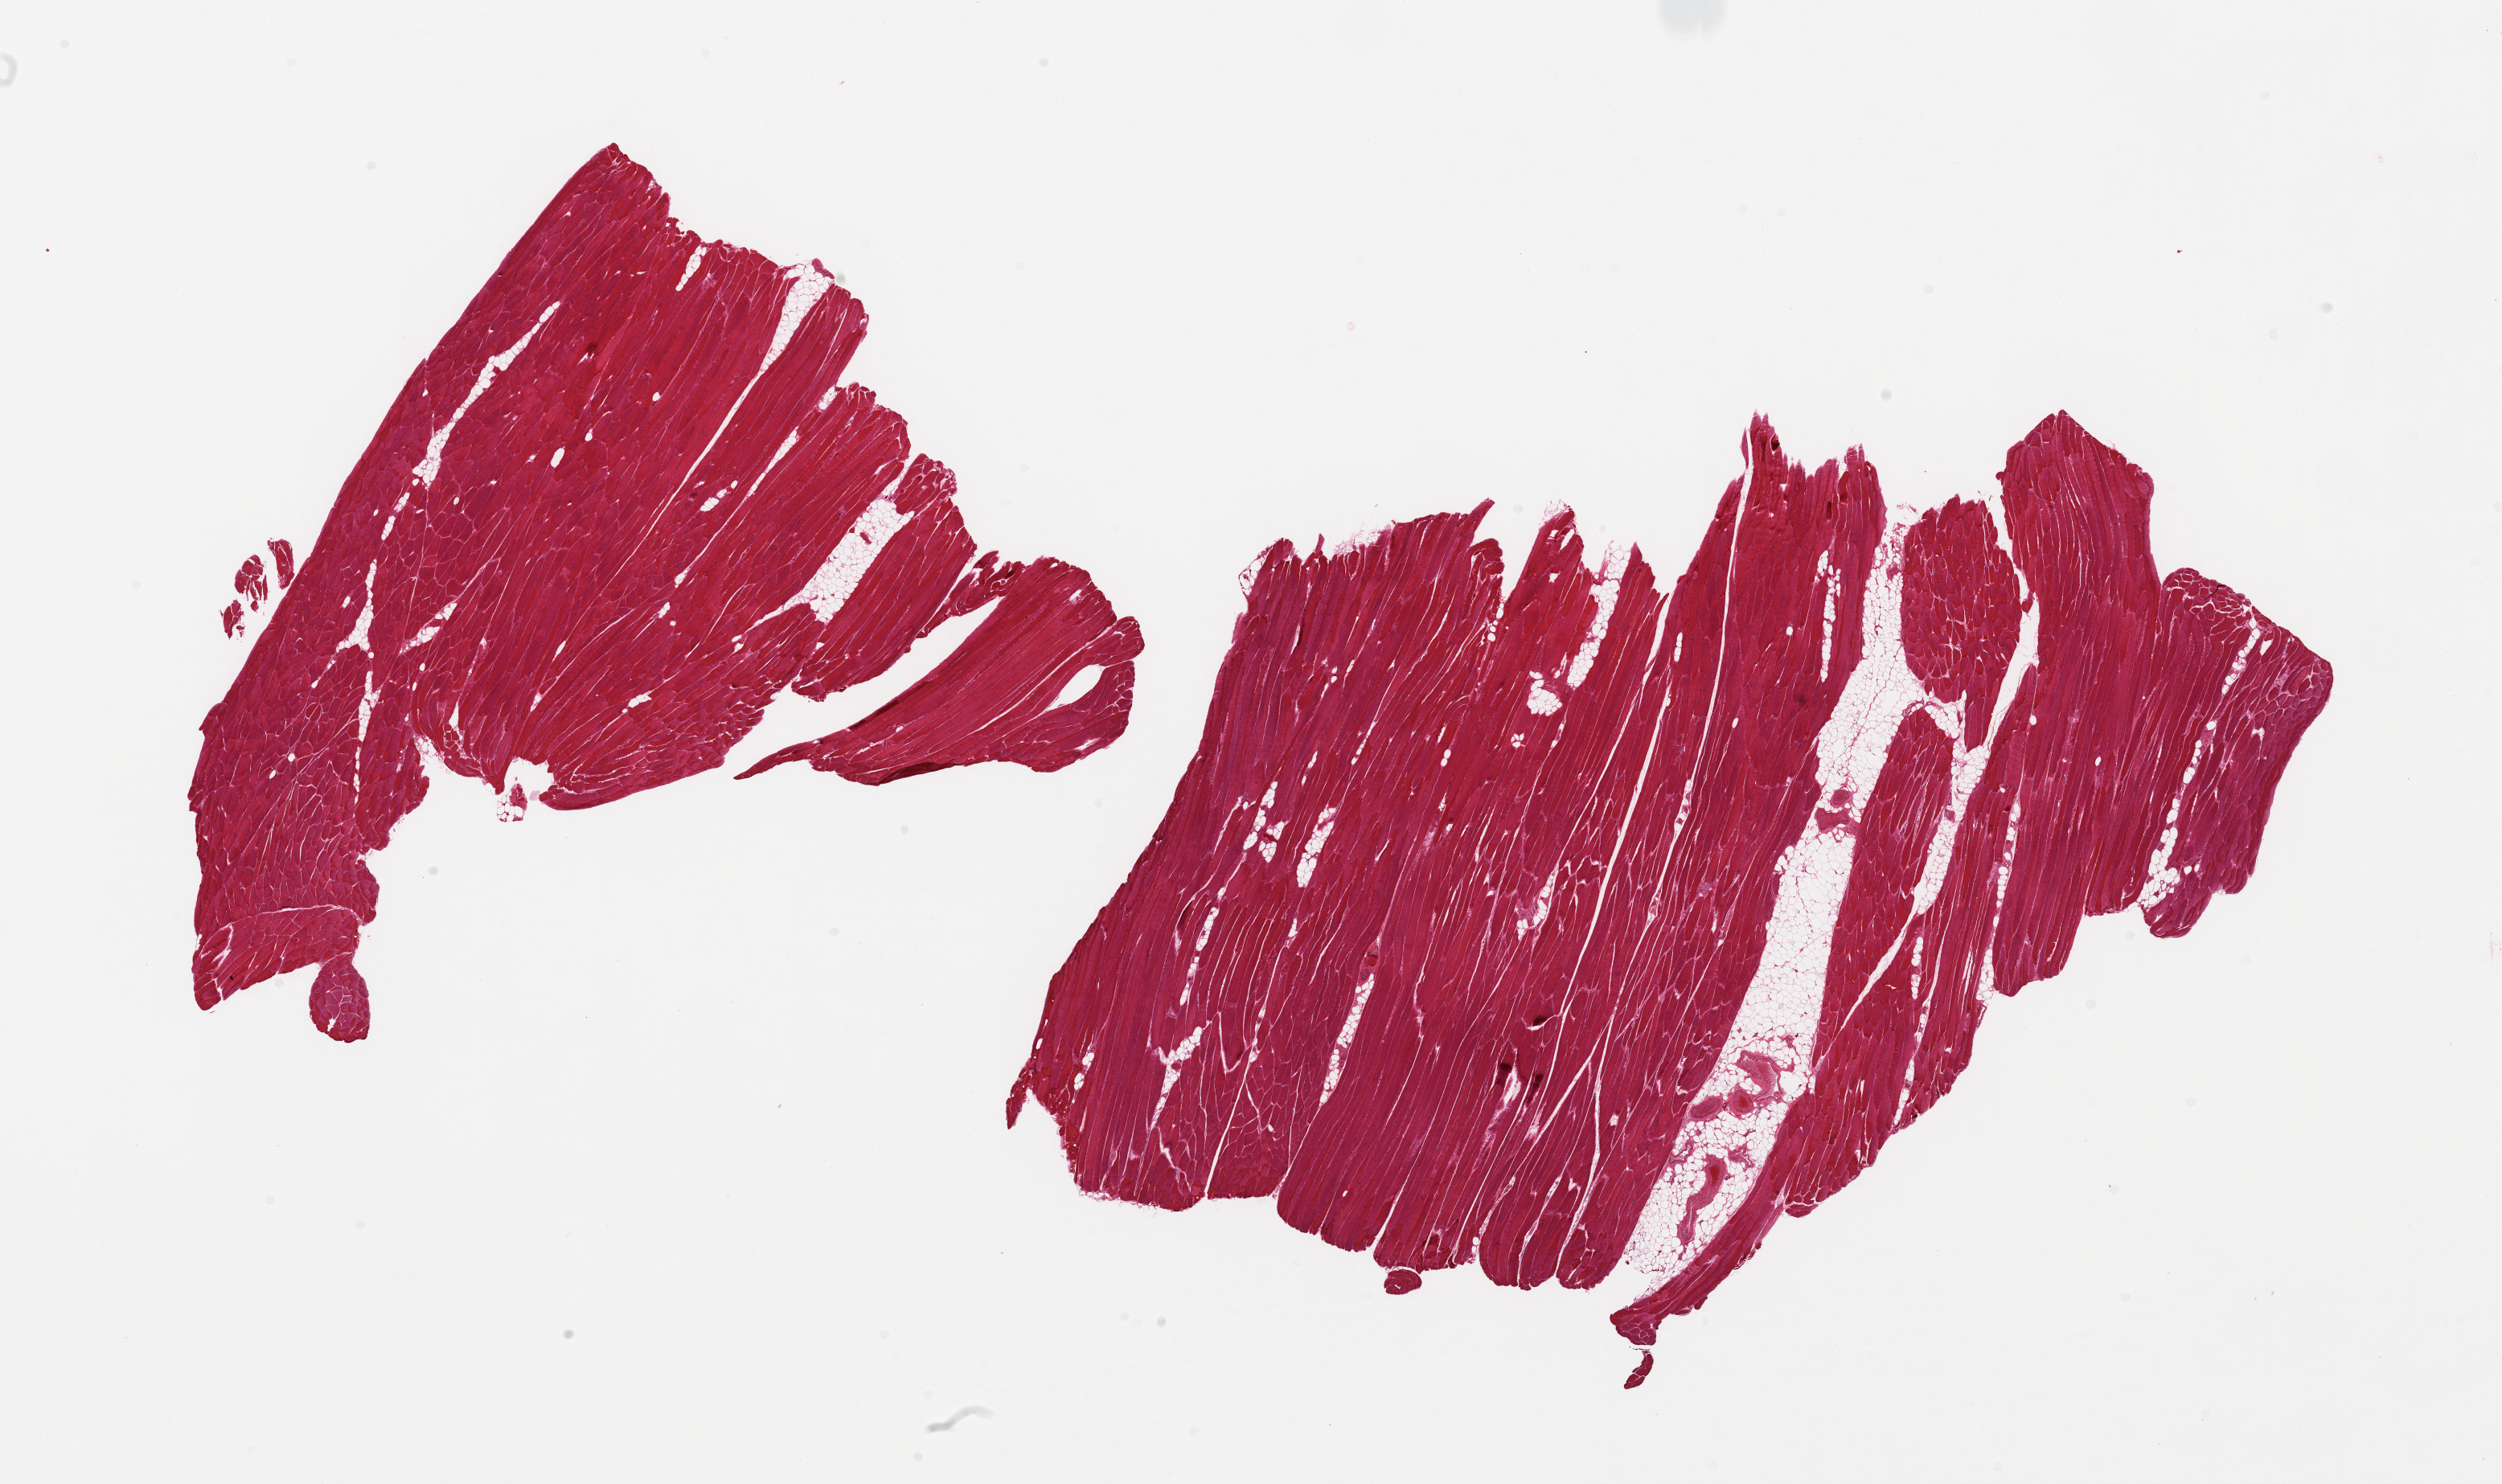
Digitized hematoxylin and eosin (H&E)-stained section, low-resolution overview of the scanned area, about 24.6 x 14.6 mm, PAXgene-fixed paraffin-embedded (PFPE) section, section of skeletal muscle (target tissue), tissue donor sample. Donor sex: male.
Review note (as recorded): 2 pieces, ~10-15% adipose tissue.